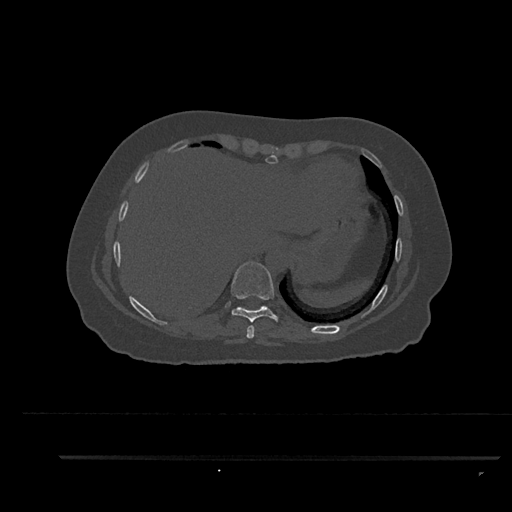
CT including the spine, one axial slice; bone window (W 1800 / L 400 HU); 512 × 512 image matrix, field of view 408 × 408 mm. Female patient, age 44 years. Case-level facts recorded for this patient, not image findings: primary cancer: renal; vertebrae with lytic lesions (as recorded): L1.
Annotated regions visible in this slice (semi-automatically segmented with operator editing):
- T8 vertebra: box from (x=246, y=325) to (x=255, y=339) px
- T9 vertebra: (x=231, y=262)–(x=279, y=323)